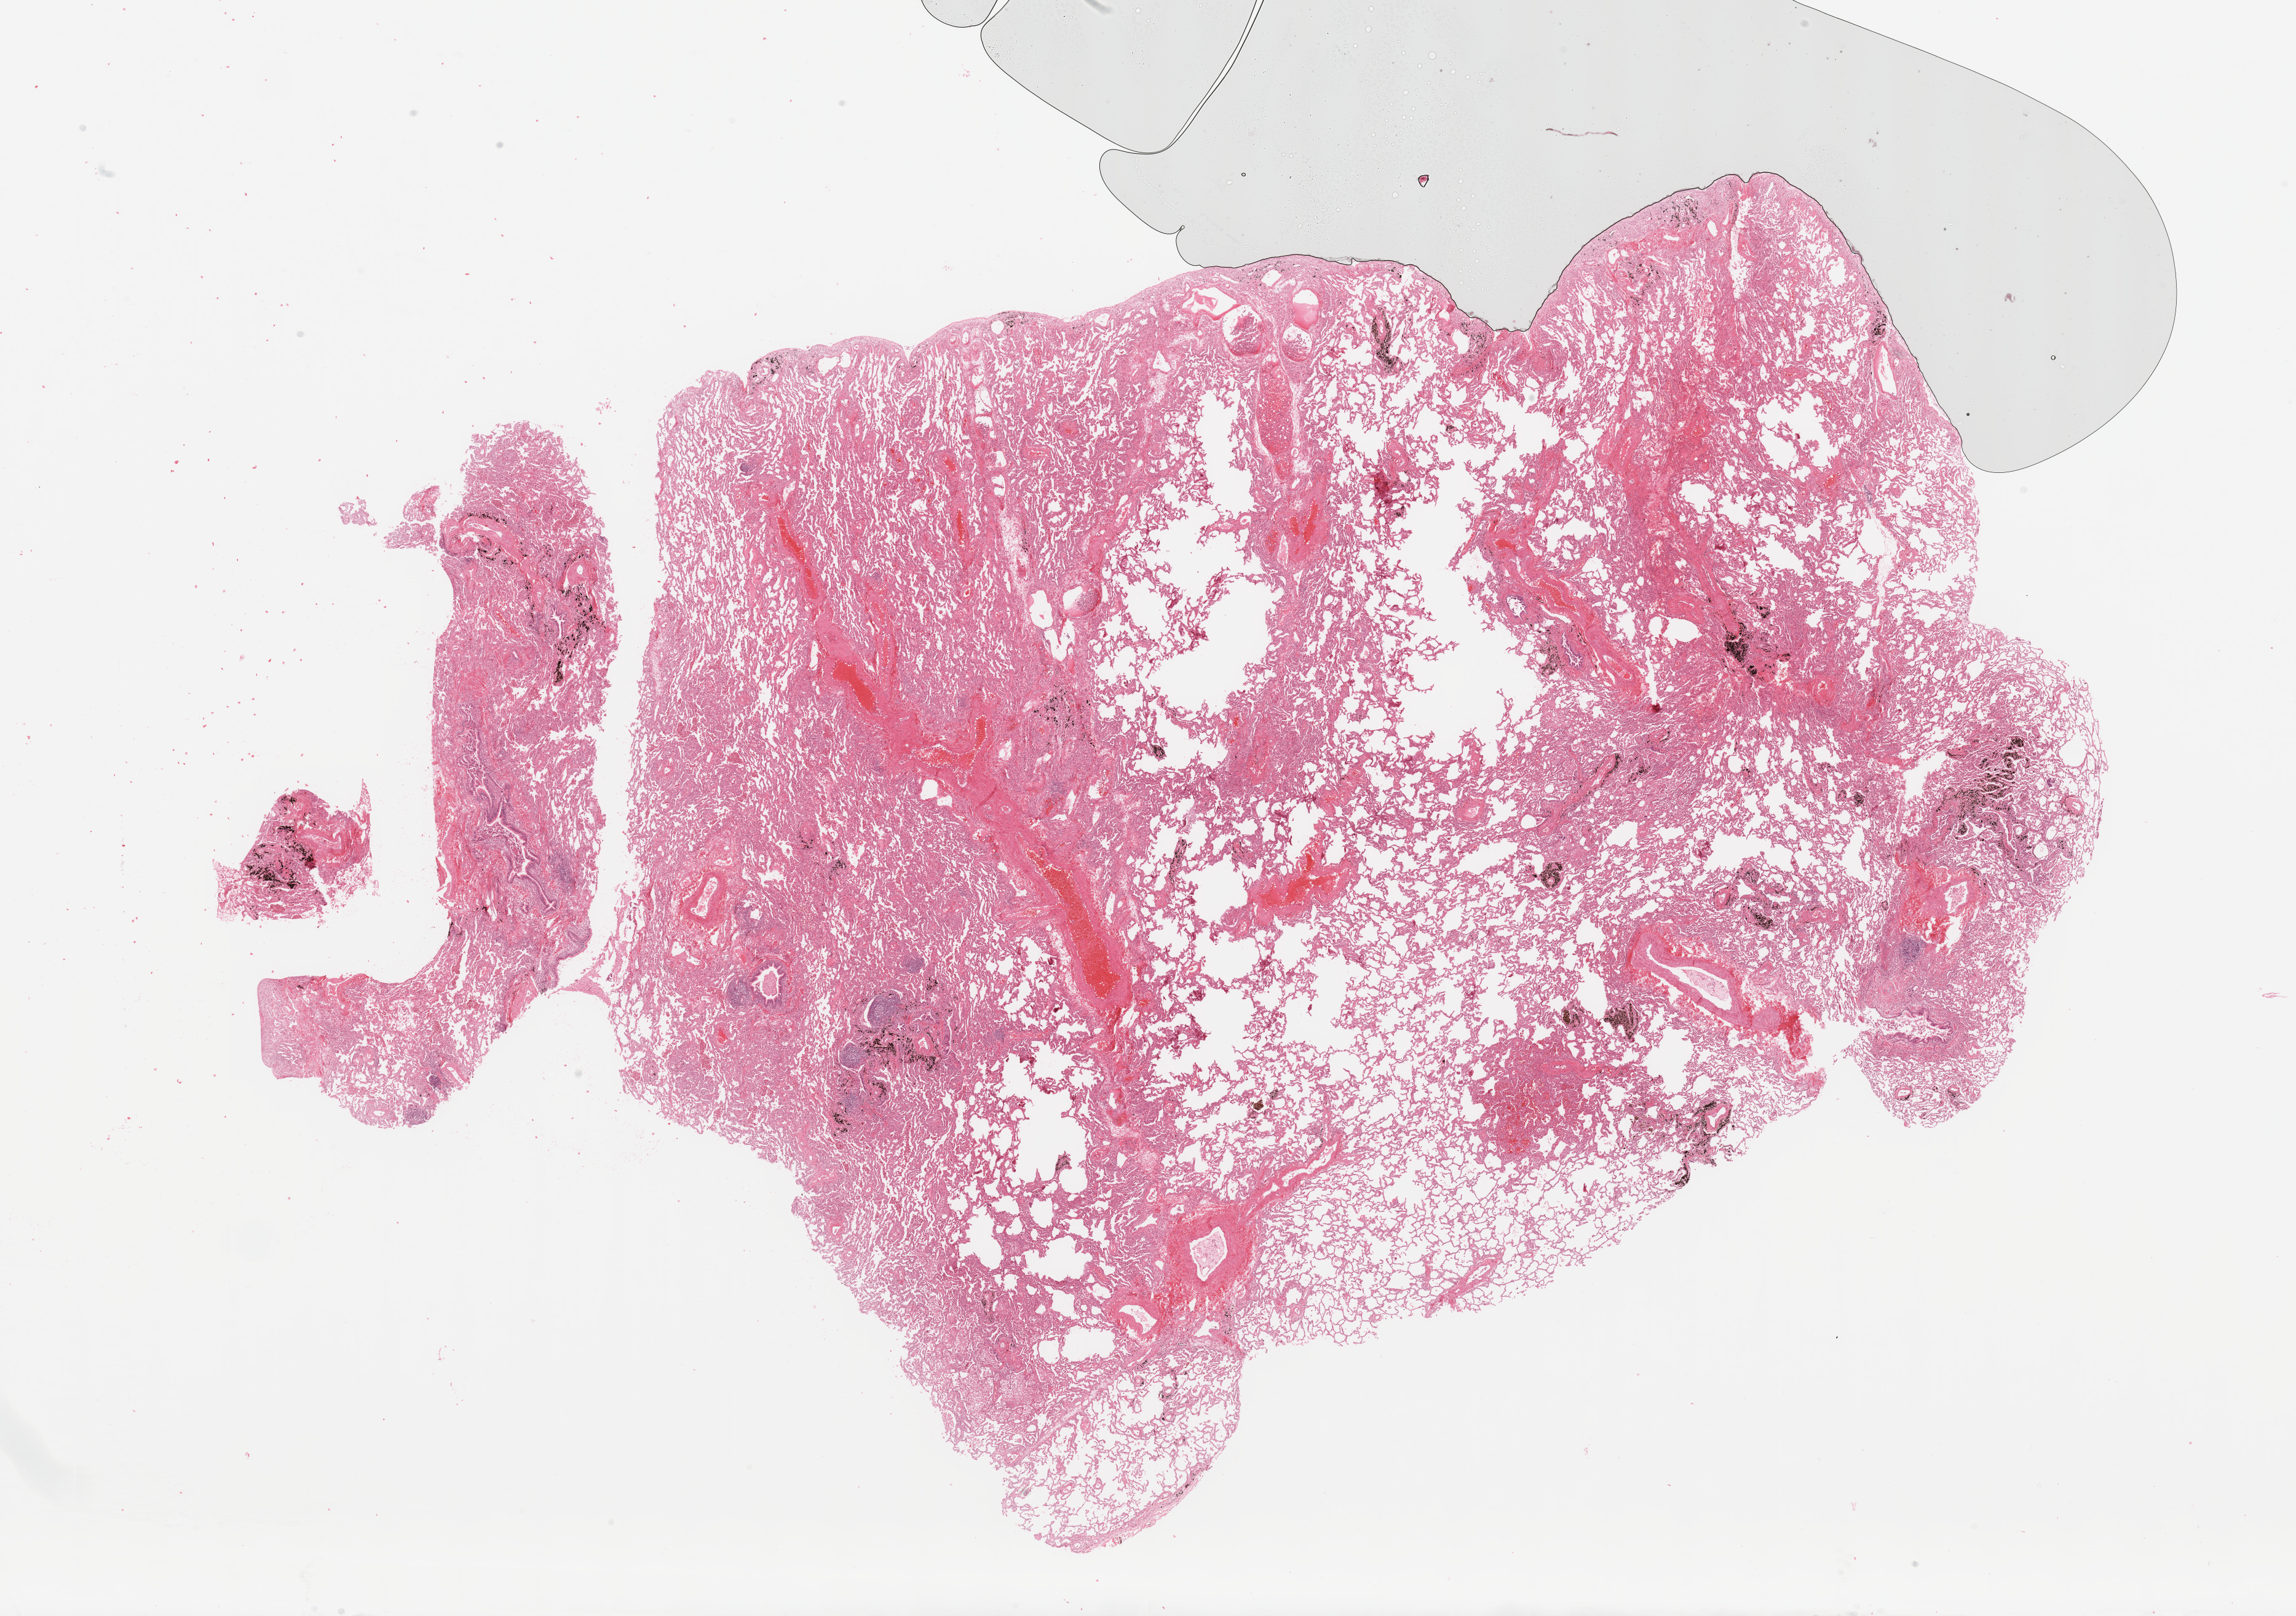
Digitized H&E tissue section (whole slide) — low-resolution overview of the scanned area, about 29.5 x 20.8 mm (from a 20x scan), lung, normal (non-tumour) tissue. 49-year-old male patient.
• this section: normal (non-tumour) tissue from the same patient
• patient diagnosis: Adenocarcinoma, NOS